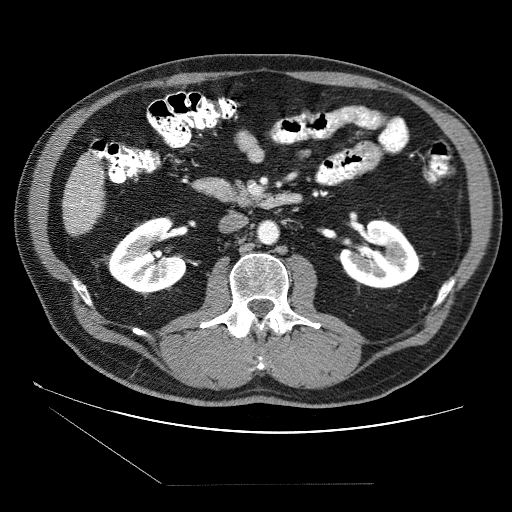
Contrast-enhanced abdominal CT (liver protocol), one axial slice. Position 10 of 87 along the scan axis. Reconstruction kernel STANDARD. Soft-tissue window (W 400 / L 40 HU). 2.5 mm slice thickness. 512 × 512 image matrix, field of view 400 × 400 mm. From the clinical record (not read from this slice): diagnosis: hepatocellular carcinoma (patient treated with transarterial chemoembolisation; whether this scan precedes or follows treatment is not stated here); TNM stage (as recorded): Stage-II; Child-Pugh class: B; tumour nodularity: multinodular; tumour size: 2.6 cm.
Structures marked on this image (semi-automatically segmented with operator editing):
- liver parenchyma outside the tumour (the mass and vessels are separate outlines, so this box may not span the whole liver): box from (x=62, y=158) to (x=106, y=234) px
- liver vessels: (x=69, y=167)–(x=98, y=216)